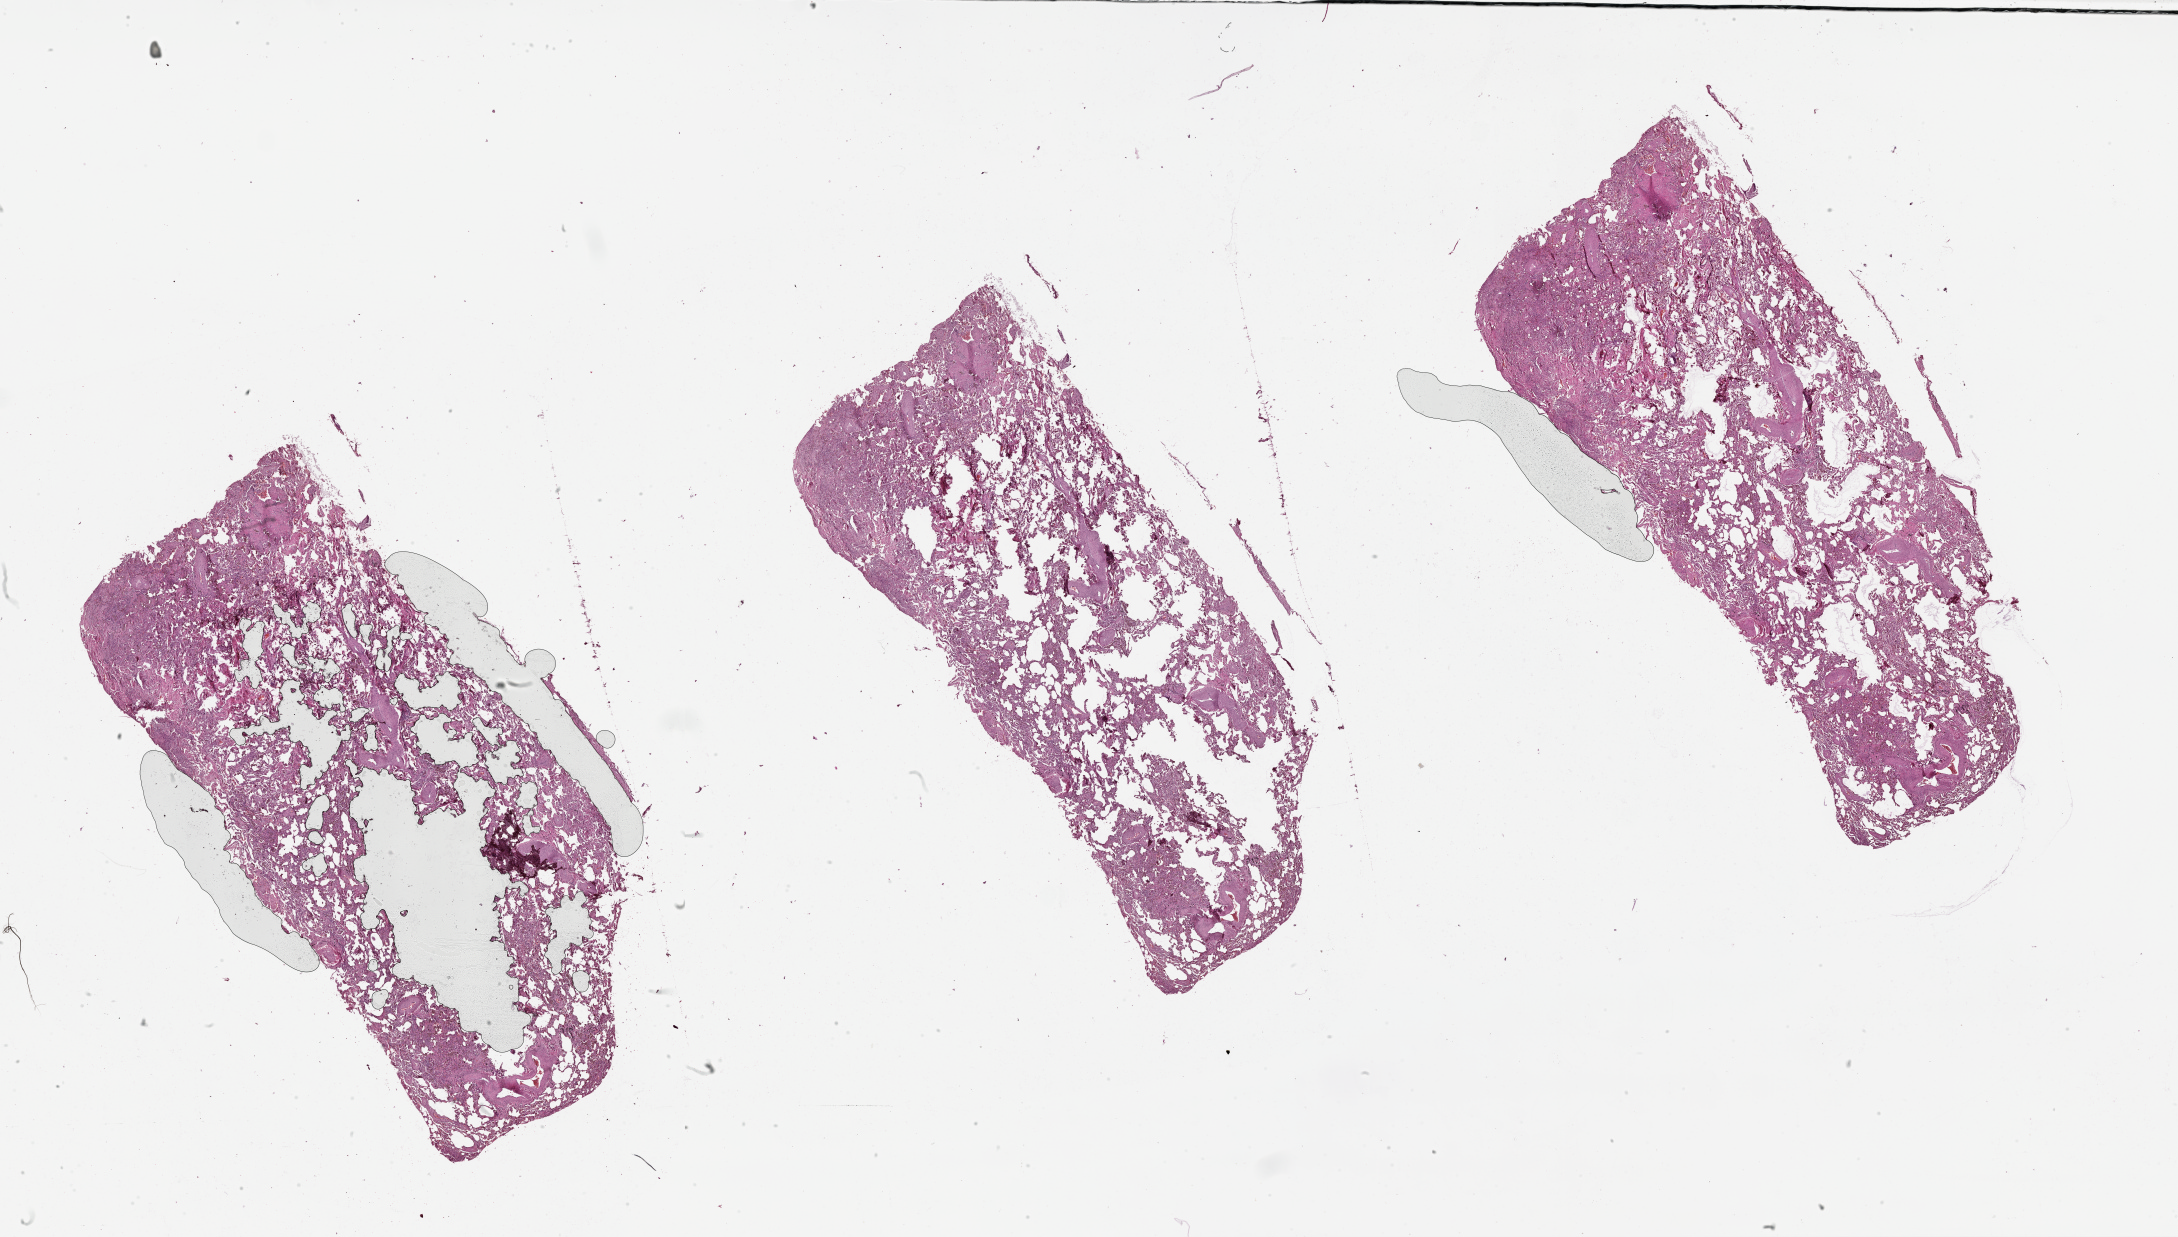
Hematoxylin and eosin (H&E) stained whole-slide image — low-resolution overview of the scanned area, about 35.1 x 19.9 mm (slide scanned at 20x). Normal (non-tumour) tissue sample, lung. Male, 63 y/o.
• this section: normal (non-tumour) tissue from the same patient
• patient diagnosis (cohort enrolment): squamous cell carcinoma (lung)